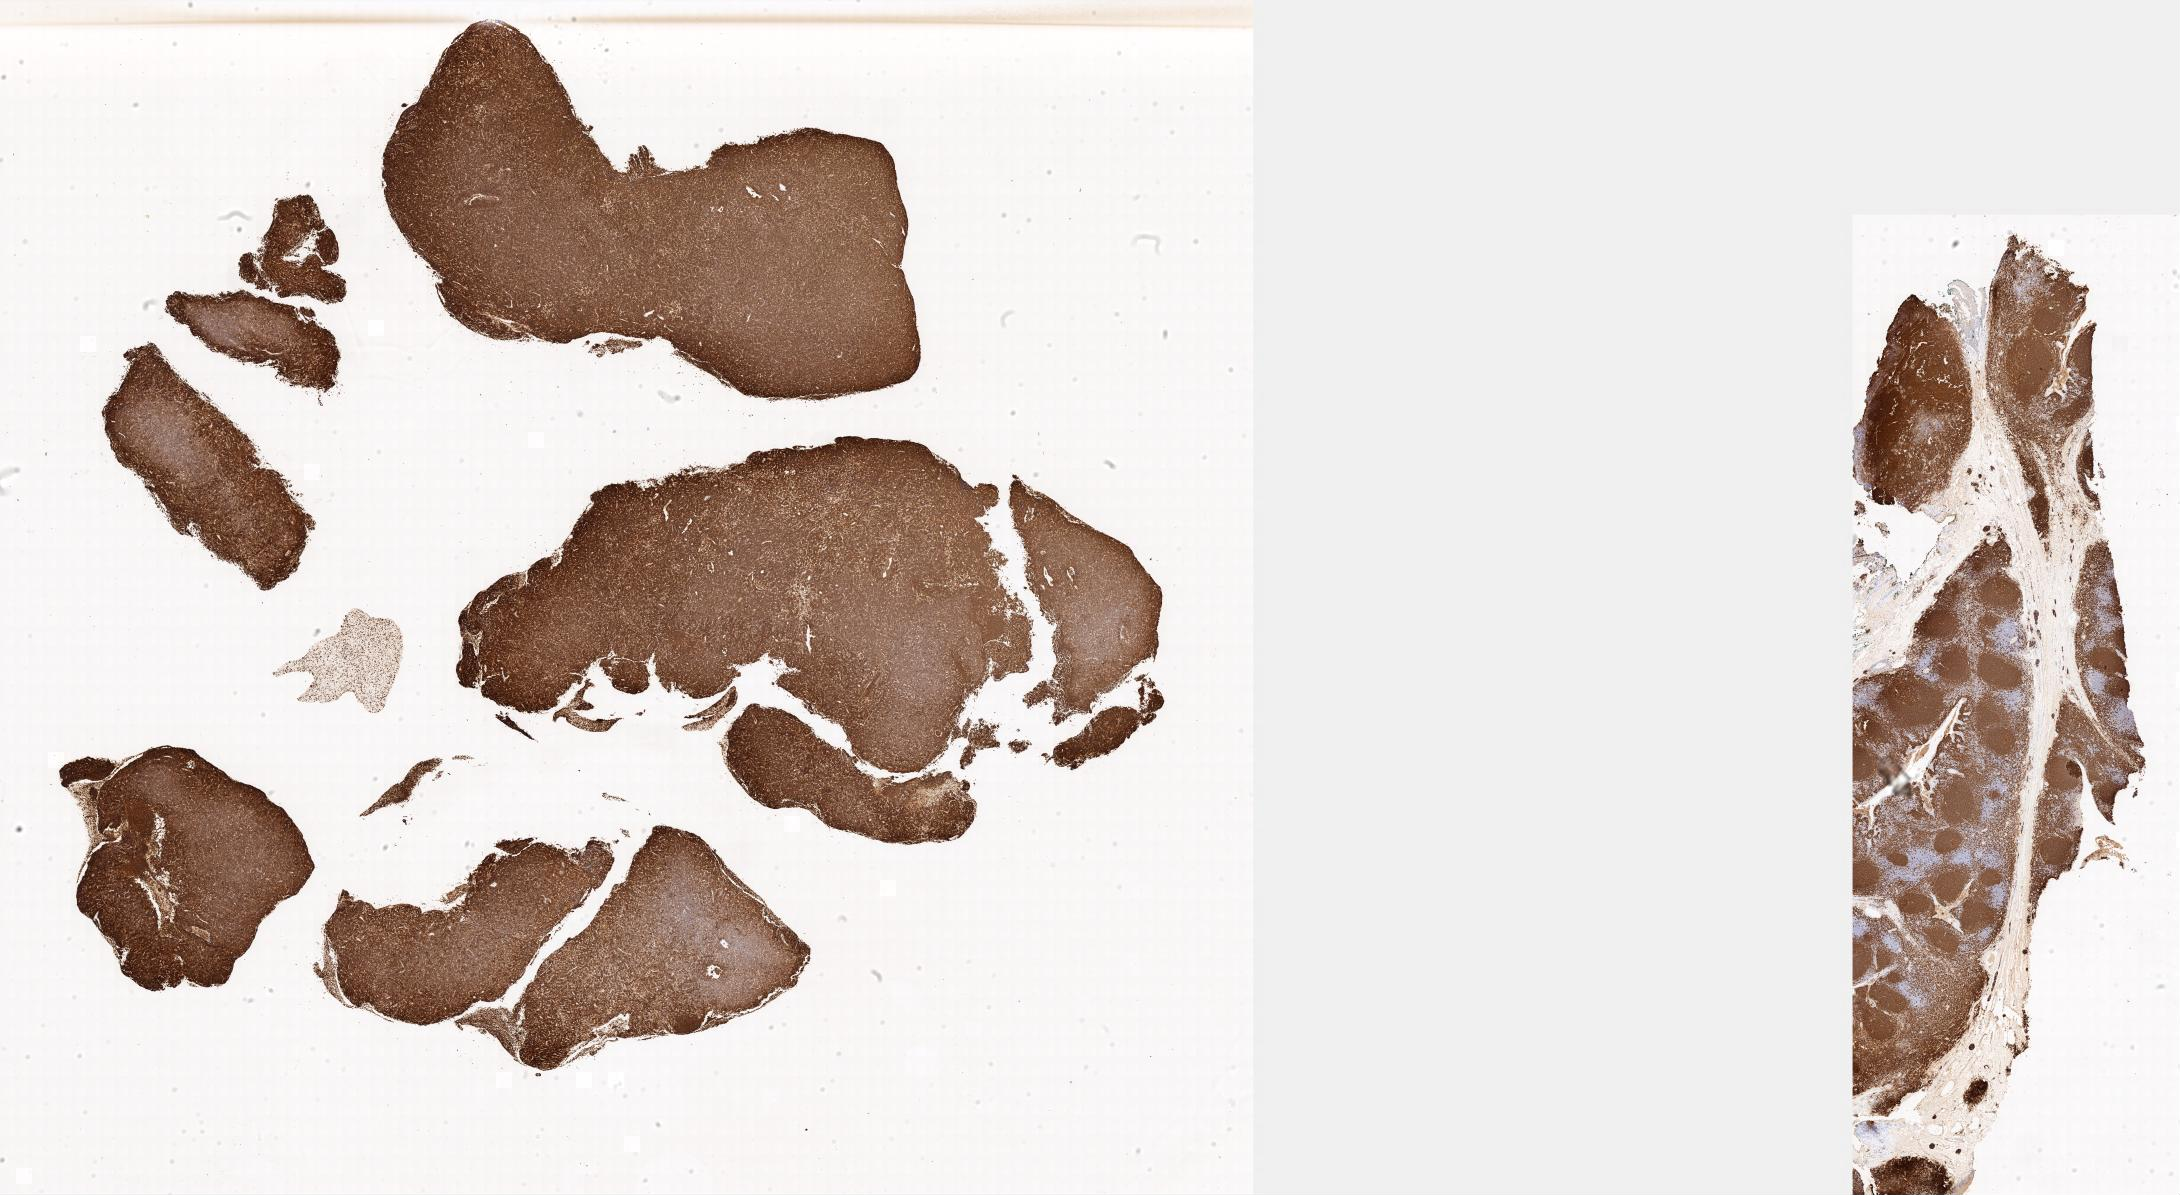
Whole-slide image, immunohistochemical stain for CD20 — whole scanned area shown as a low-resolution overview; specimen: tumor tissue; anatomic site: soft tissue. Female, age 9 years at initial diagnosis.
Diagnosis: Burkitt lymphoma, NOS.